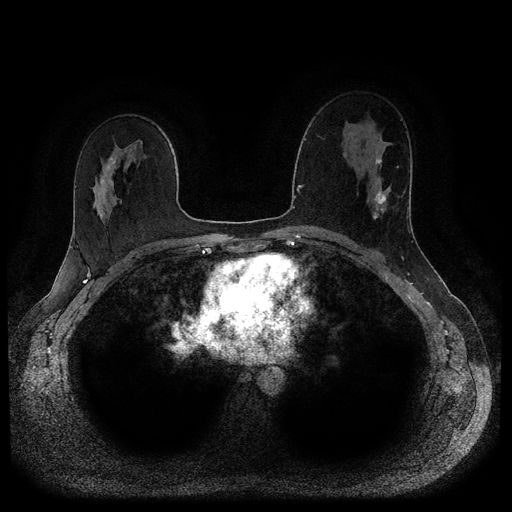
Breast MRI (dynamic contrast-enhanced, multi-phase), one axial slice. Position 60 of 116 along the scan axis. Dynamic contrast-enhanced series, time point 2 of 5 at this slice position (early post-contrast). 1.5 T. TE 2.6 ms, TR 5.3 ms. 2 mm slice thickness. 512 × 512 image matrix, field of view 350 × 350 mm. Female patient, age 45 years.
Outlined on this slice (semi-automatically segmented with operator editing):
- breast lesion (labelled 'tumour' in the annotation; benign lesions carry a separate 'benign' label): bounding box <375,158,386,209> (left, top, right, bottom; pixels)